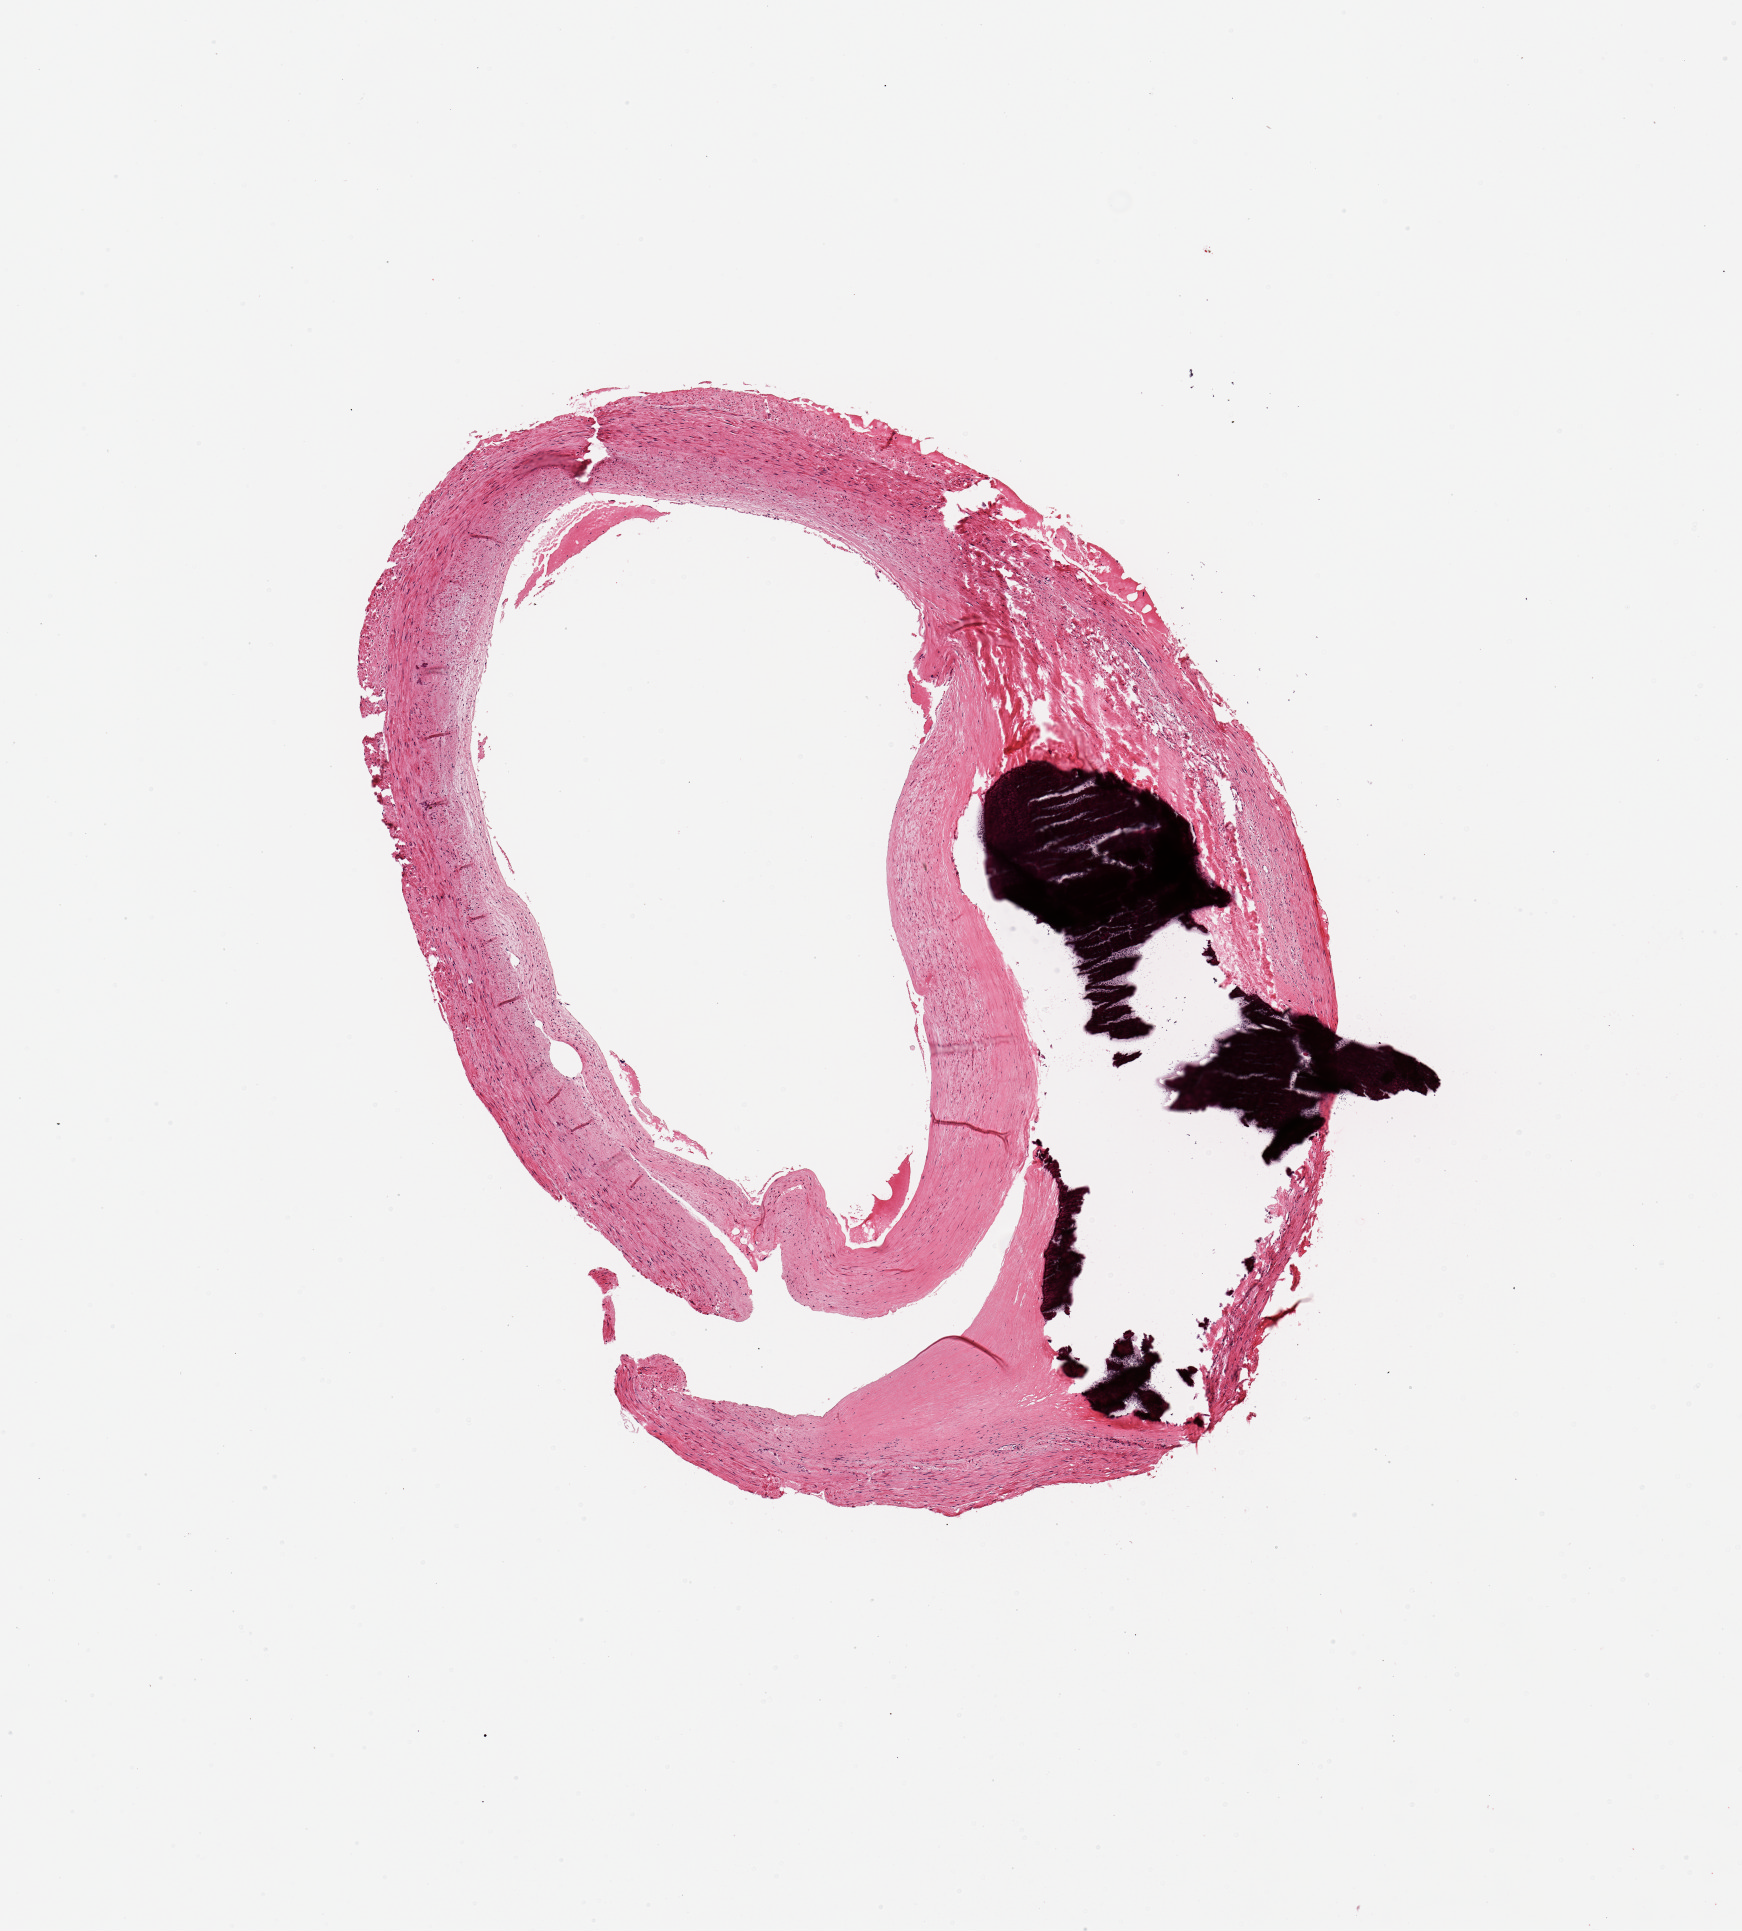
Digitized H&E-stained section, brightfield, whole scanned area (about 6.9 x 7.6 mm, slide scanned at 20x) shown as a low-resolution overview. PAXgene-fixed paraffin-embedded (PFPE) section. Section of coronary artery (target tissue). Tissue donor sample. Donor: male.
Reviewer comment on this tissue sample: 1 piece, ~50% occlusive calcified atherosis.